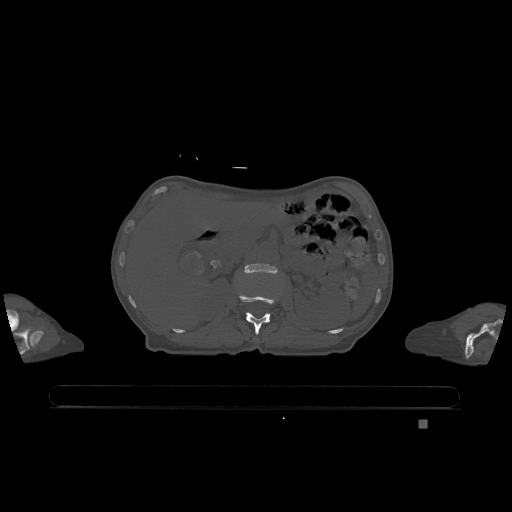
CT including the spine, one axial slice; position 462 of 1317 along the scan axis; bone window (W 1800 / L 400 HU); 0.5 mm slice thickness; 512 × 512 image matrix, field of view 500 × 500 mm. Patient: female, 74 years. Case-level facts recorded for this patient, not image findings: primary cancer: lung.
Outlined on this slice (semi-automatic segmentation, software-assisted and operator-edited):
- L1 vertebra: bounding box (x1, y1, x2, y2) in pixels: (239, 294, 278, 335)
- L2 vertebra: (245, 263, 278, 274)